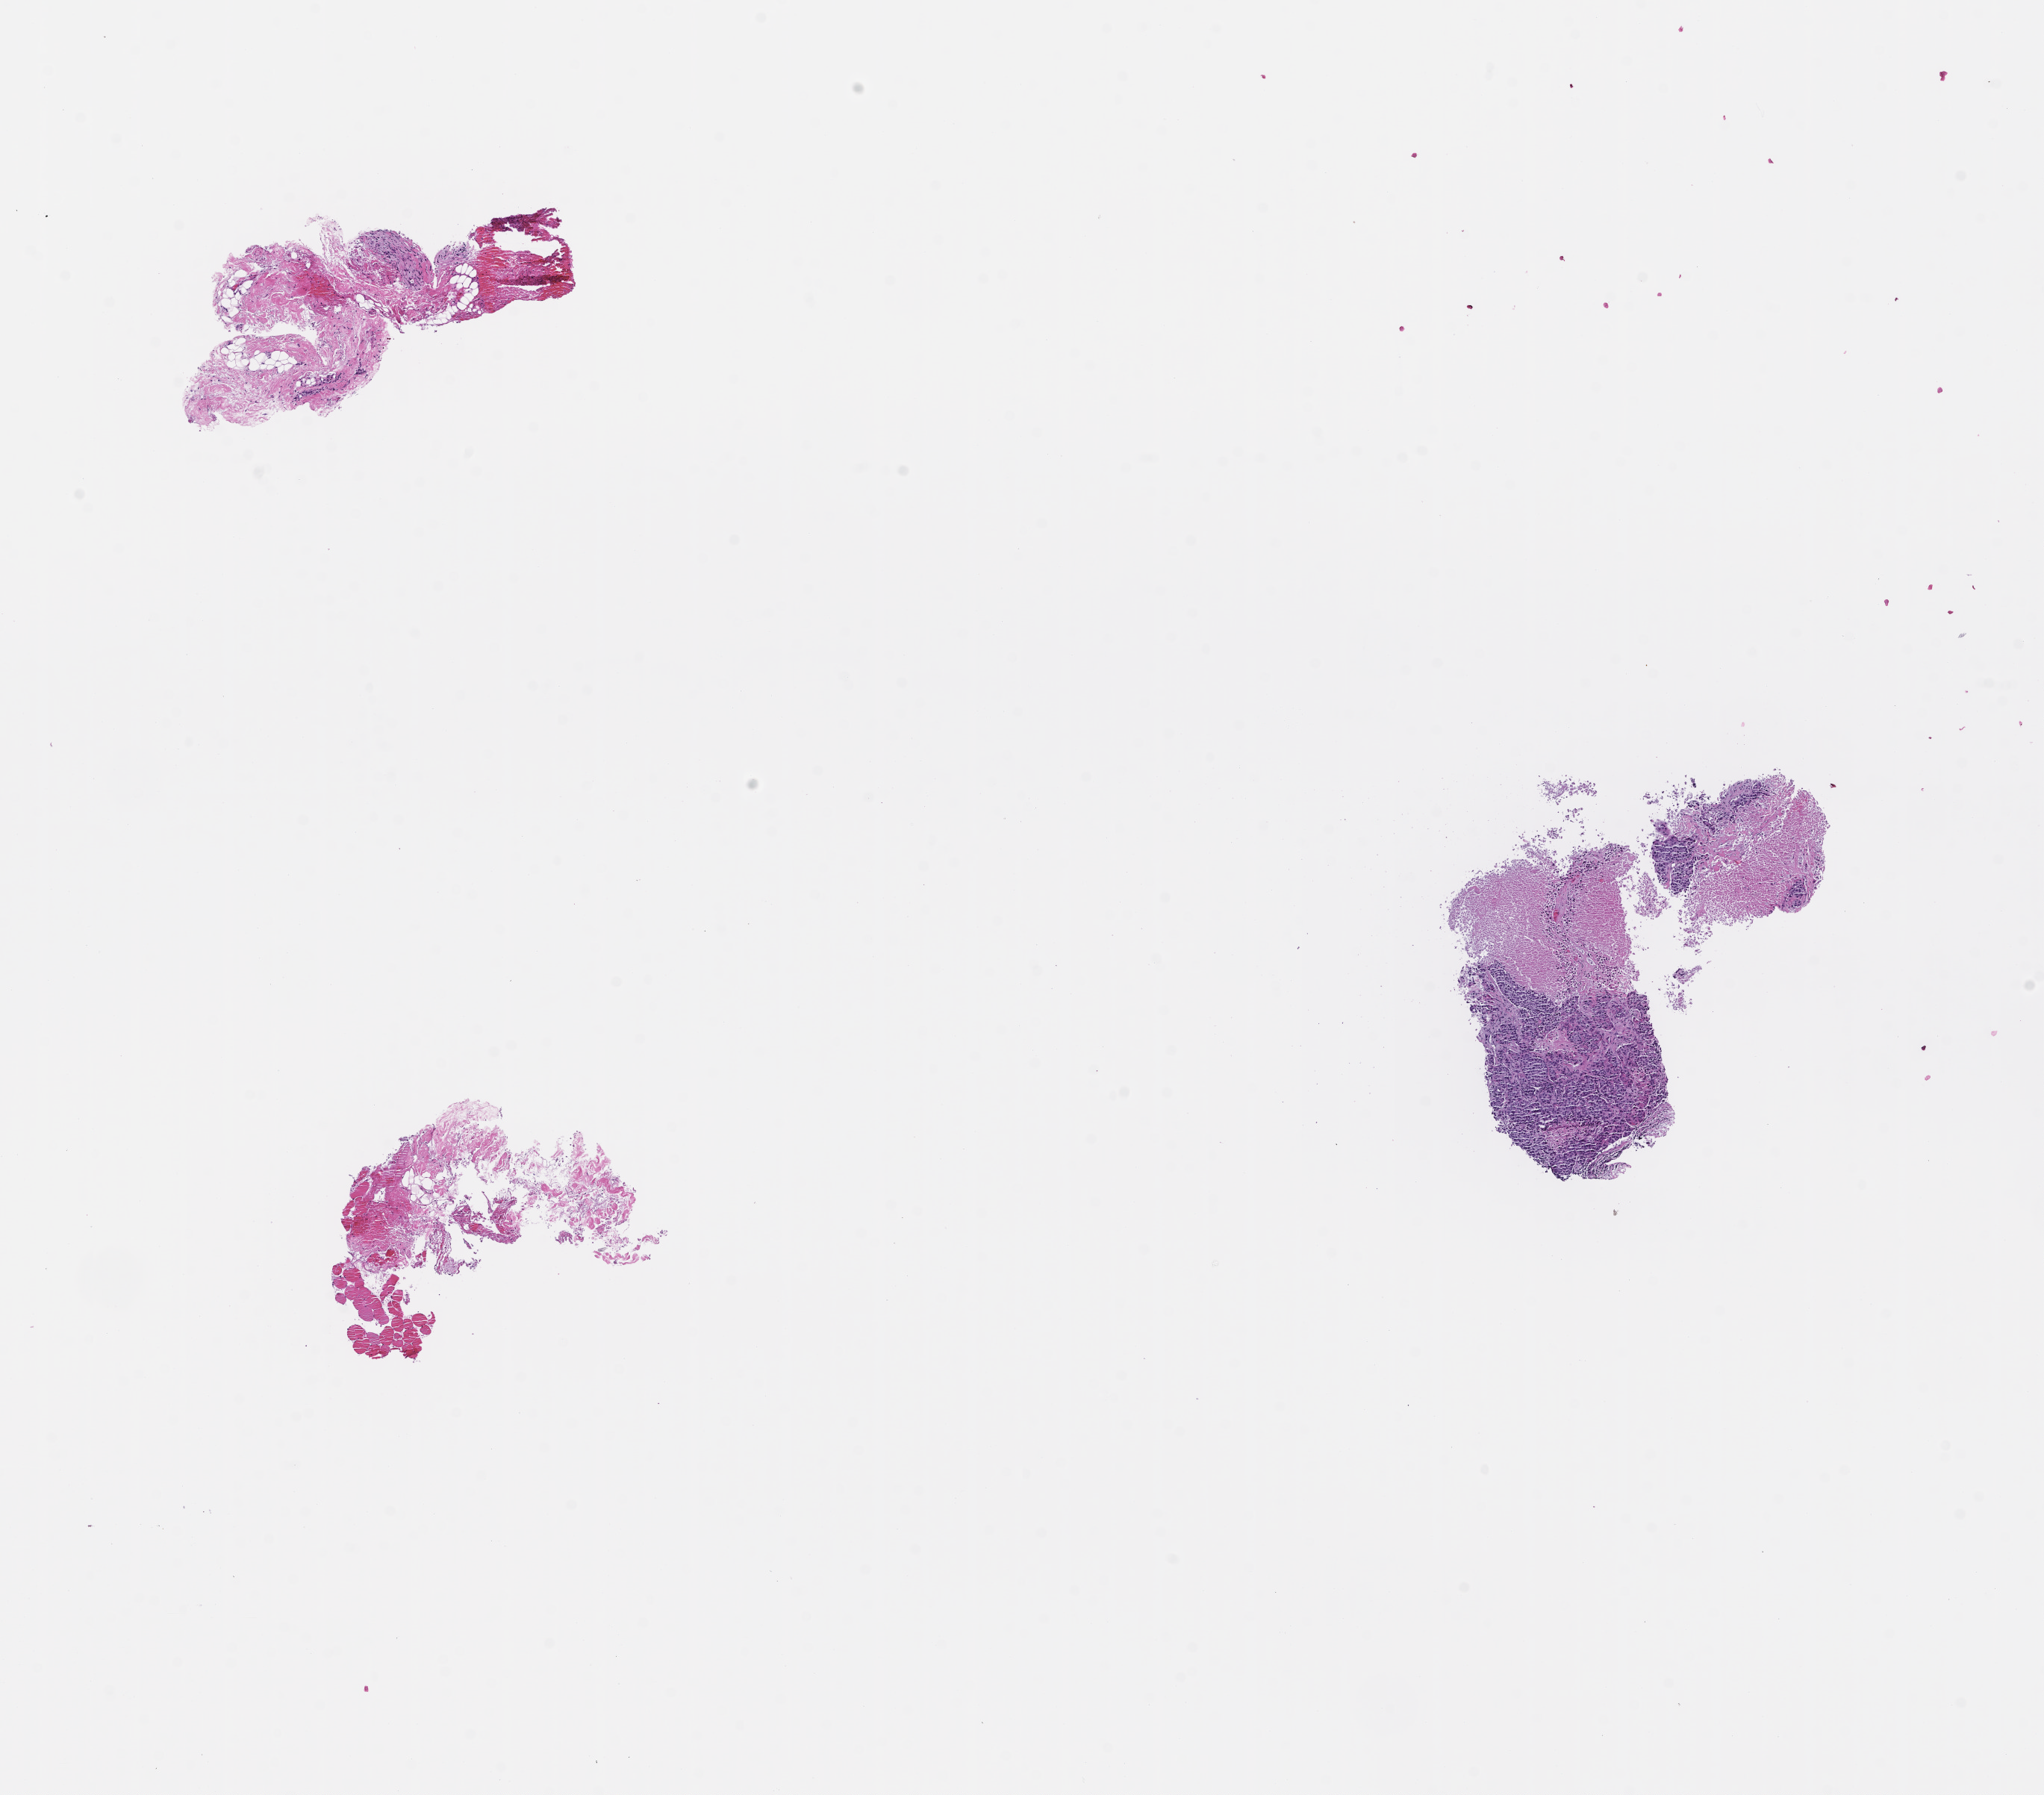
H&E whole-slide image — shown as a low-resolution overview of the whole scanned area (about 11.1 x 9.7 mm). Formalin-fixed paraffin-embedded section. Specimen time point: collected at baseline (before treatment). Patient sex: female.
This section: metastasis (sampled organ not recorded). Patient diagnosis (primary): Non-Small Cell Lung Carcinoma.